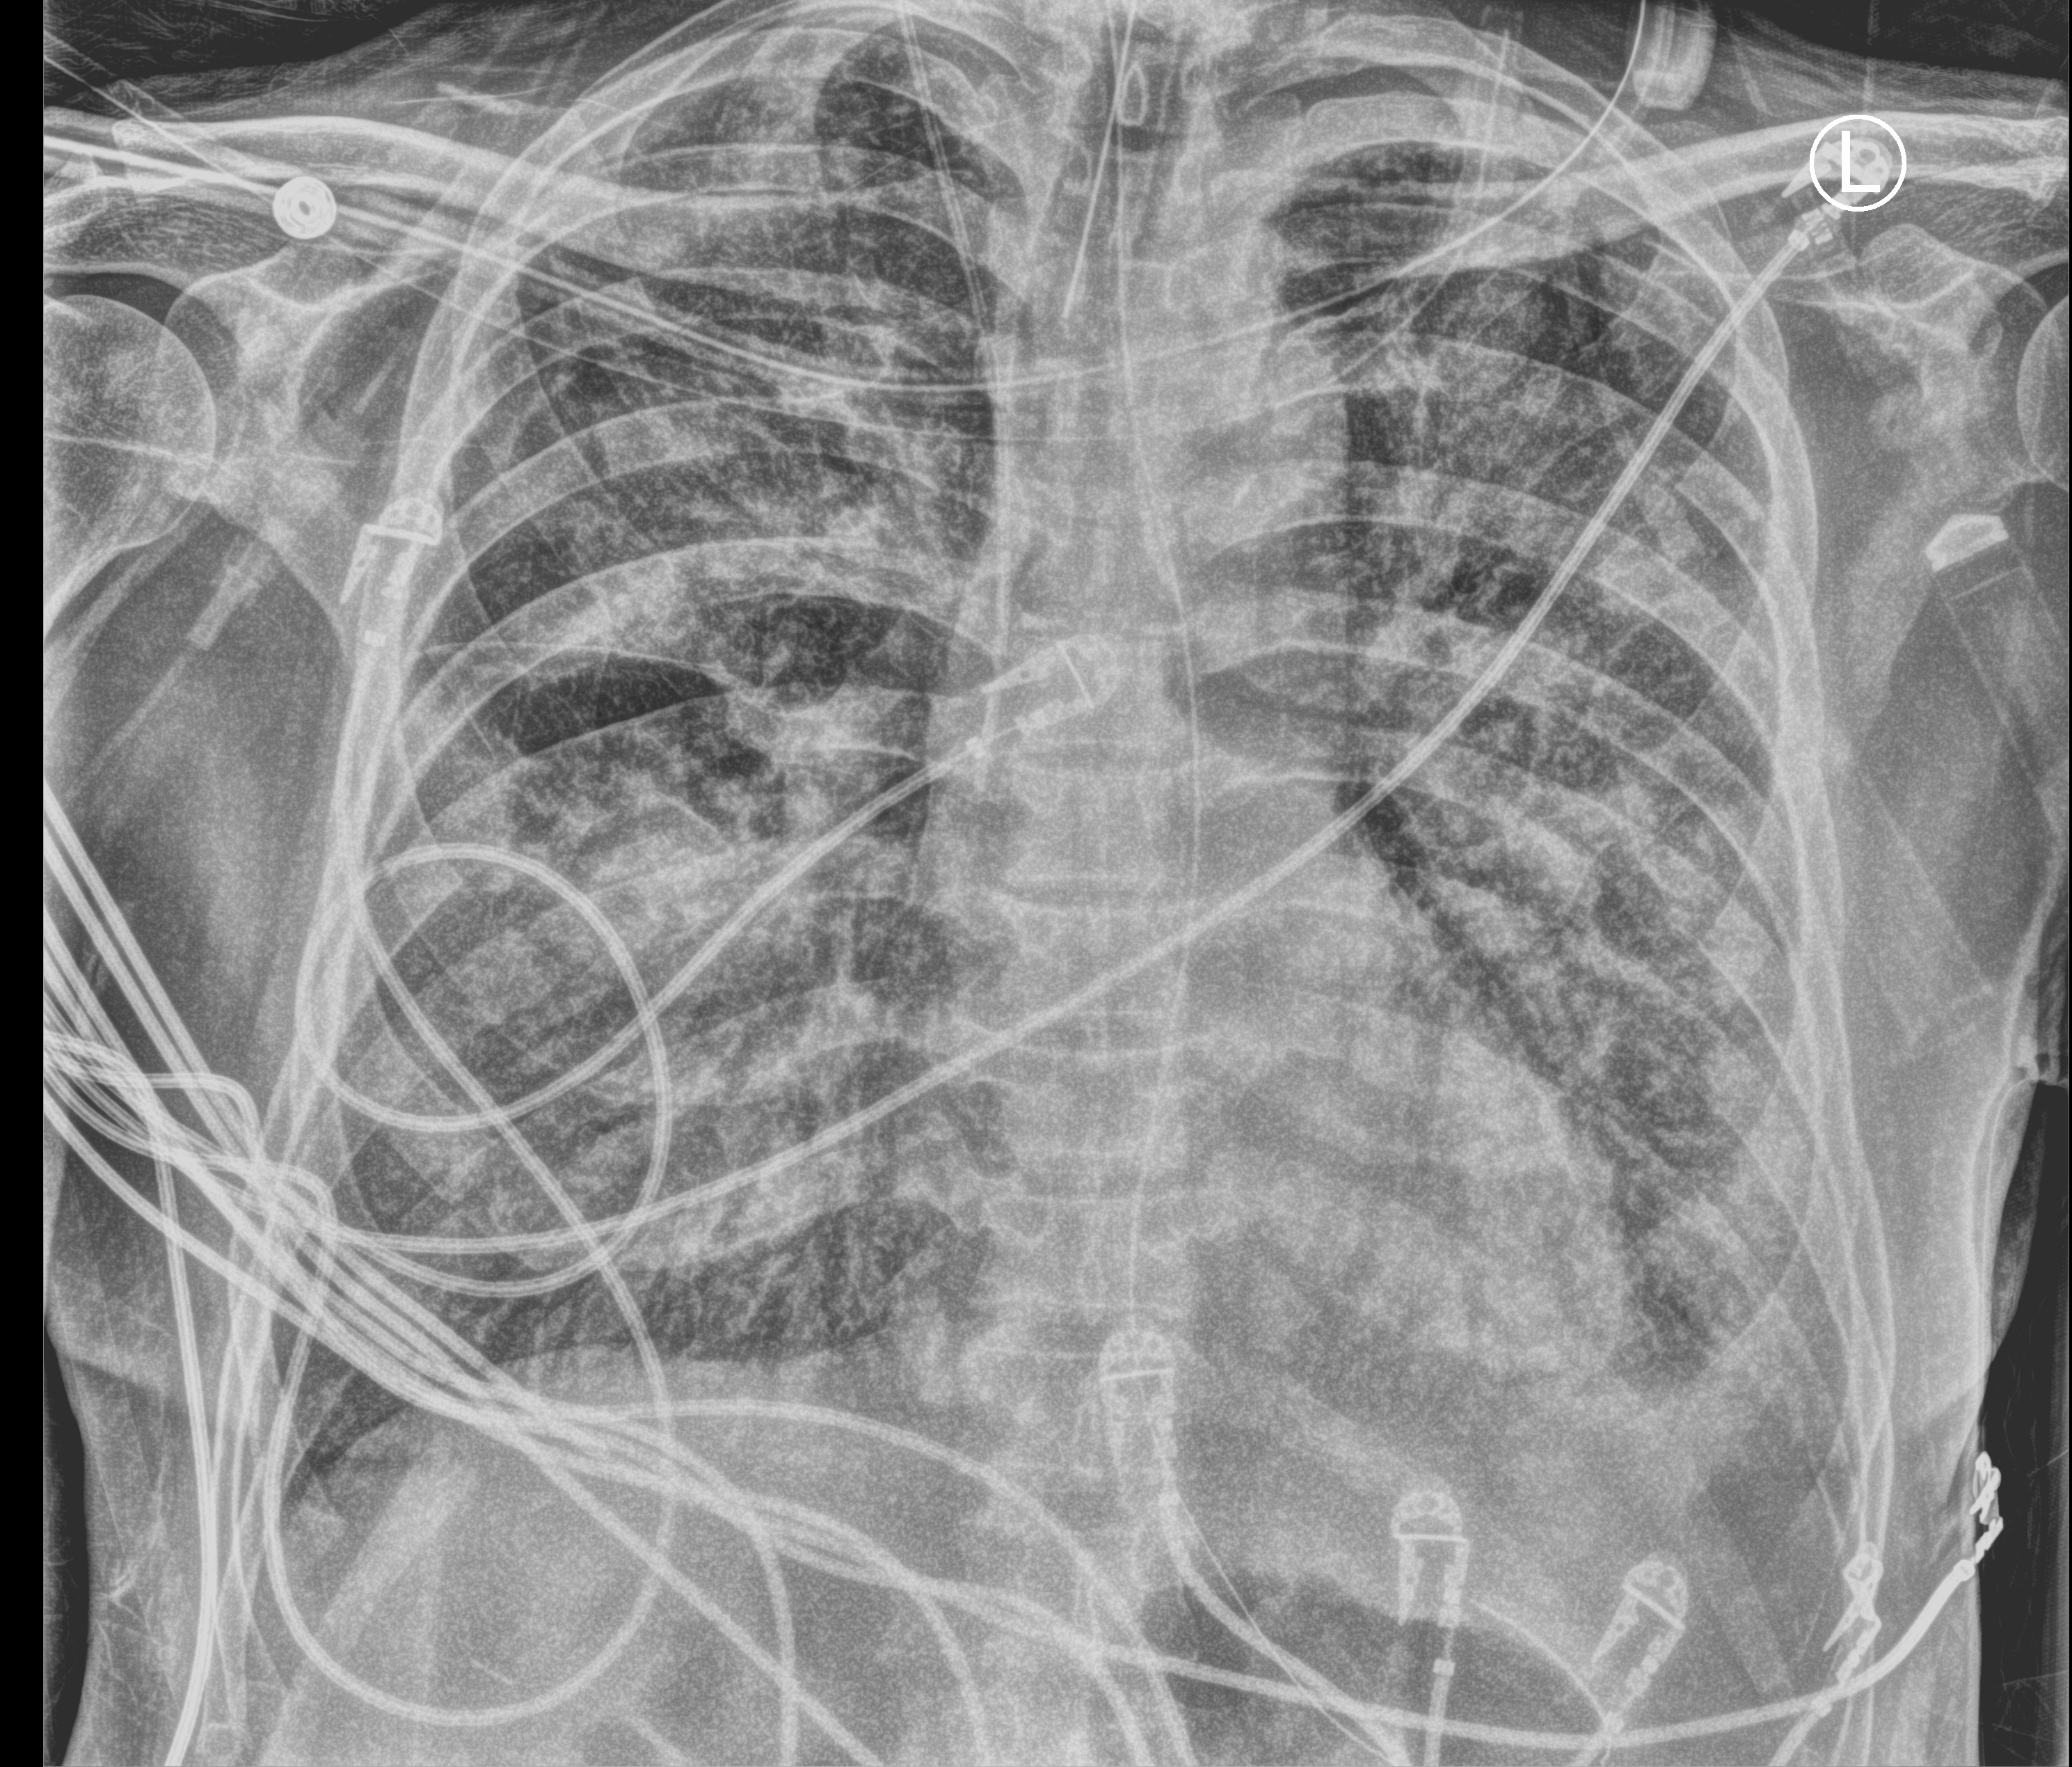
Portable chest radiograph. Male patient hospitalised with COVID-19, age 60–74 years.
From the hospital-stay record, not from the radiograph (when in the stay this image was taken is not recorded): admitted to intensive care during this hospital stay: yes.